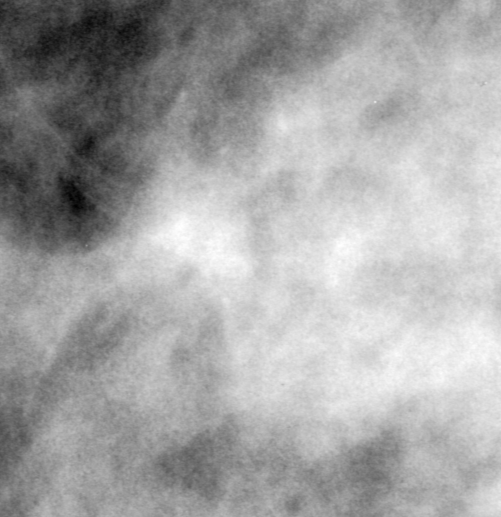
Cropped region of a digitized screen-film mammogram centred on a radiologist-marked abnormality; right breast; MLO view; BI-RADS breast density category 3 (scale 1–4).
Calcifications, morphology punctate, distribution clustered; BI-RADS assessment category 0 (incomplete: needs additional imaging); pathology (as recorded): benign.